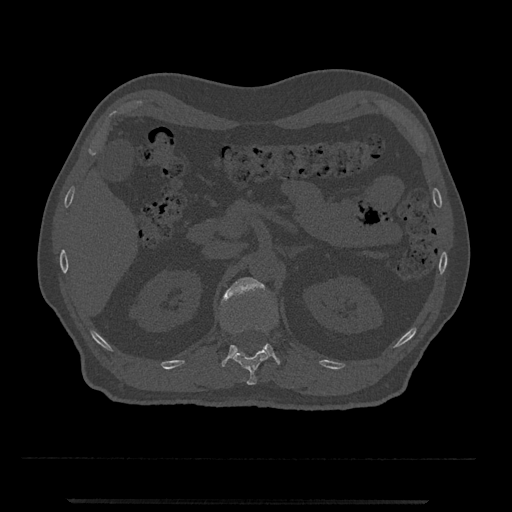
CT including the spine, one axial slice; slice 372 of 797 in the series (ordered by position); 120 kVp; bone window (W 1800 / L 400 HU); 0.5 mm slice thickness; 512 × 512 image matrix. Patient: male, 63 years. Case-level facts recorded for this patient, not image findings: primary cancer: prostate.
Outlined on this slice (semi-automatically segmented with operator editing):
- L1 vertebra: box from (x=222, y=277) to (x=280, y=367) px
- T12 vertebra: (x=231, y=325)–(x=270, y=385)